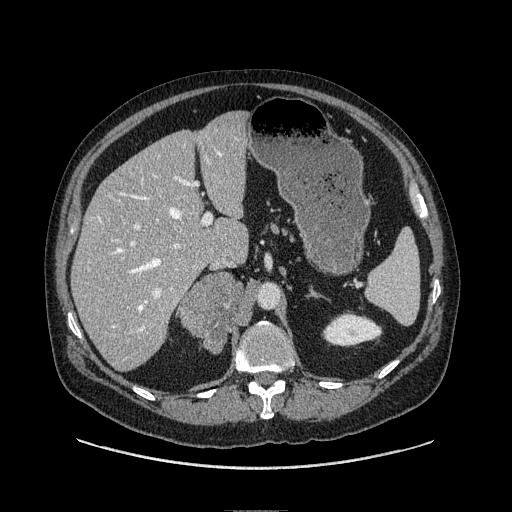
Contrast-enhanced abdominal CT, one axial slice; slice 59 of 149 in the series (ordered by position); soft-tissue window (W 400 / L 40 HU); 1.25 mm slice thickness; 512 × 512 image matrix. Male patient. From the clinical record (not read from this slice): diagnosis: adrenocortical carcinoma; tumour side: right adrenal; tumour size at pathology: 7.5 cm; Ki-67 index: 15 %; stage (as recorded): 2.
Annotated regions visible in this slice (semi-automatically segmented with operator editing):
- mass: bounding box <180,269,247,354> (left, top, right, bottom; pixels)